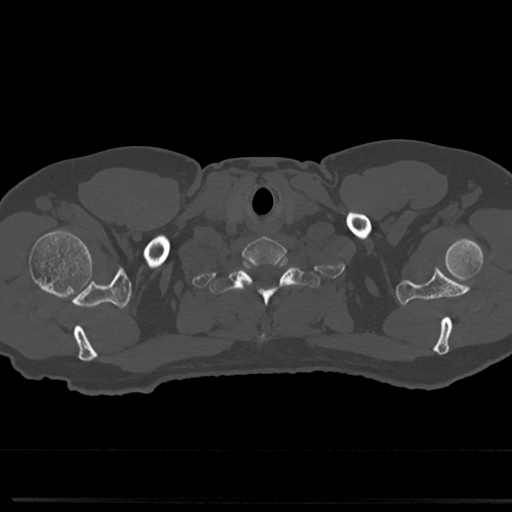
CT including the spine, one axial slice; position 685 of 817 along the scan axis; 120 kVp; bone window (W 1800 / L 400 HU); 0.5 mm slice thickness; 512 × 512 image matrix. Patient: male, 61 years. From the clinical record (not read from this slice): primary cancer: prostate.
Annotated regions visible in this slice (semi-automatically segmented with operator editing):
- T1 vertebra: bounding box [x1, y1, x2, y2] px = [215, 260, 316, 345]